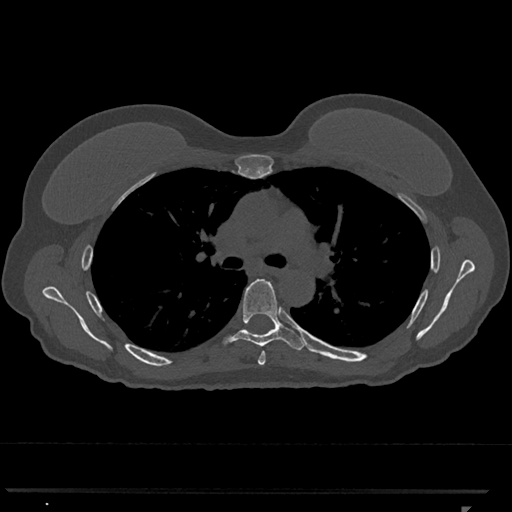
CT including the spine, one axial slice; position 767 of 793 along the scan axis; reconstruction kernel Br40s/3; 120 kVp; bone window (W 1800 / L 400 HU); 512 × 512 image matrix, field of view 380 × 380 mm. Female patient, age 62 years. From the clinical record (not read from this slice): primary cancer: renal.
Outlined on this slice (semi-automatic segmentation, software-assisted and operator-edited):
- T5 vertebra: box from (x=258, y=351) to (x=266, y=365) px
- T6 vertebra: (x=222, y=279)–(x=304, y=350)